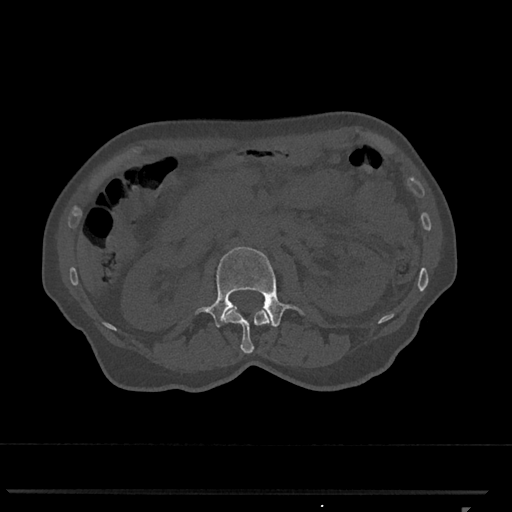
CT including the spine, one axial slice; slice 362 of 793 in the series (ordered by position); 120 kVp; bone window (W 1800 / L 400 HU); 0.5 mm slice thickness; 512 × 512 image matrix, field of view 380 × 380 mm. Female patient, age 62 years. From the clinical record (not read from this slice): primary cancer: renal.
Outlined on this slice (semi-automatically segmented with operator editing):
- L1 vertebra: bounding box [x1, y1, x2, y2] px = [224, 308, 273, 354]
- L2 vertebra: [196, 247, 304, 327]